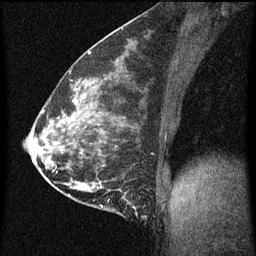
Breast MRI (dynamic contrast-enhanced), one sagittal slice; position 27 of 60 along the scan axis; dynamic contrast-enhanced series, image 2 of 3 at this slice position (ordered by acquisition); 1.5 T; TE 4.2 ms, TR 8 ms; 2 mm slice thickness; 256 × 256 image matrix, field of view 180 × 180 mm. Female patient, age 35 years.
Outlined on this slice (semi-automatically segmented with operator editing):
- analysis volume of interest (the breast-tissue region the enhancement analysis was run in; not a lesion): bounding box [x1, y1, x2, y2] px = [110, 178, 148, 219]
- tumour enhancement mask (voxels above the 70 % enhancement threshold inside the analysis volume of interest): [124, 196, 137, 211]